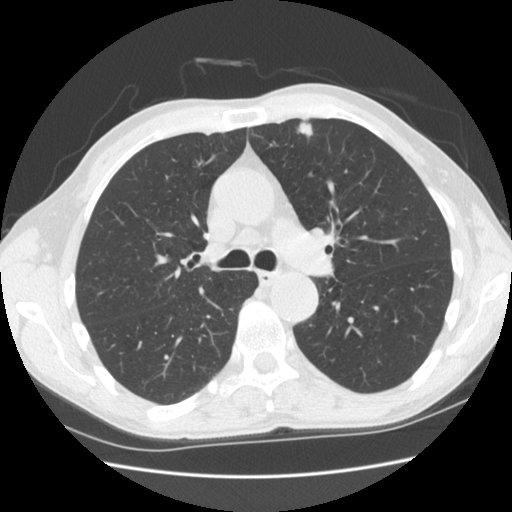
Low-dose screening chest CT, one axial slice; position 110 of 169 along the scan axis; lung window (W 1500 / L -600 HU); 2.5 mm slice thickness; 512 × 512 image matrix, field of view 340 × 340 mm.
Structures marked on this image (outlined manually by an expert reader):
- lesion 1 (tumor, upper lobe of left lung): bounding box (x1, y1, x2, y2) in pixels: (297, 122, 313, 137)